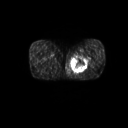
FDG PET of an extremity soft-tissue mass (from a PET/CT study), one axial slice. Slice 21 of 267 in the series (ordered by position). 128 × 128 image matrix. Patient: male, 59 years. From the clinical record (not read from this slice): histological type: pleiomorphic liposarcoma; grade: high; site of the primary tumour: left thigh.
Outlined on this slice (expert contour drawn on MRI and transferred to this co-registered scan by the dataset authors):
- gross tumour volume including surrounding oedema: bounding box <71,54,91,74> (left, top, right, bottom; pixels)
- gross tumour volume (mass): <72,56,88,73>